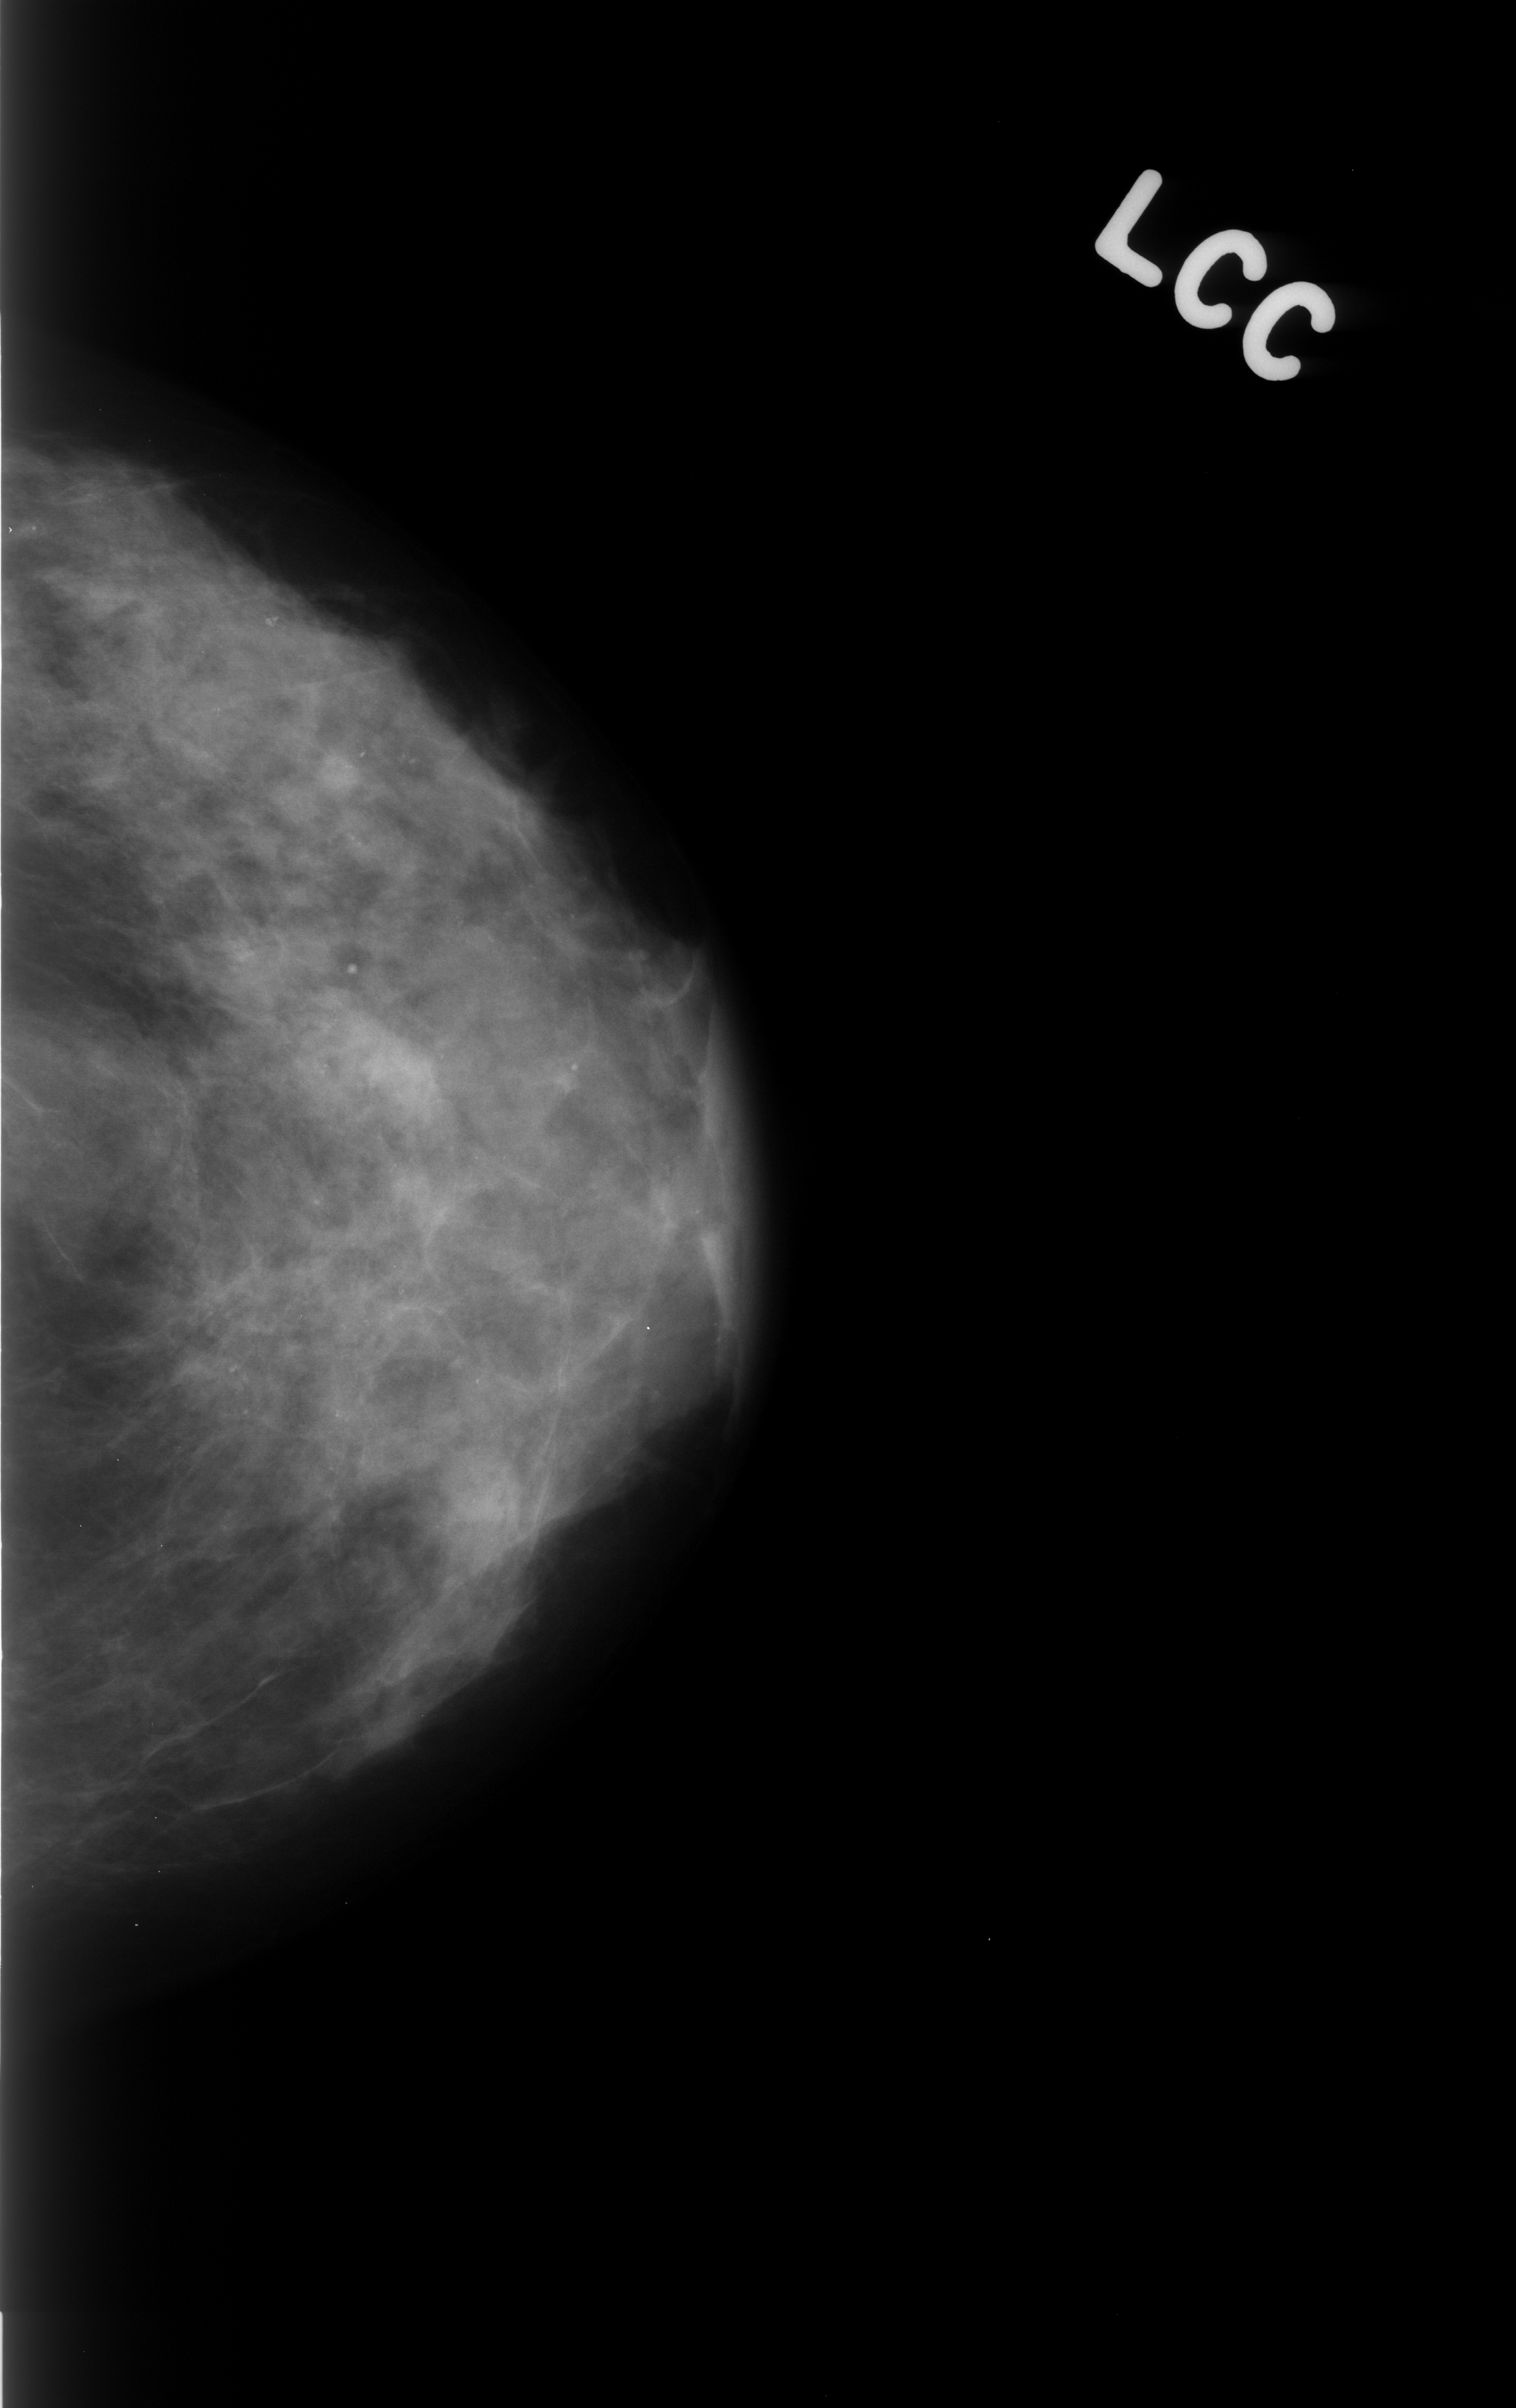
Digitized screen-film mammogram. Left breast. Craniocaudal (CC) view. 1516 × 2408 image matrix.
Expert-marked regions of interest on this film, with their recorded descriptors:
- calcifications, morphology pleomorphic, distribution diffusely scattered; BI-RADS assessment category 3; pathology result (as recorded, not read from the image): benign: box from (x=0, y=459) to (x=685, y=1699) px